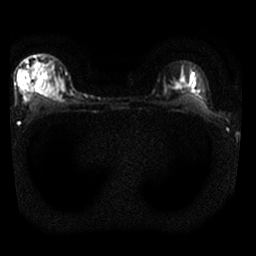
Breast MRI, one axial slice; position 22 of 25 along the scan axis; diffusion-weighted series; image 2 of 4 stored at this slice position (different b-values; order by instance number); 1.5 T; 256 × 256 image matrix. Female patient.
Annotated regions visible in this slice (manually delineated by an expert):
- tumour on diffusion-weighted imaging: bounding box <36,79,50,94> (left, top, right, bottom; pixels)